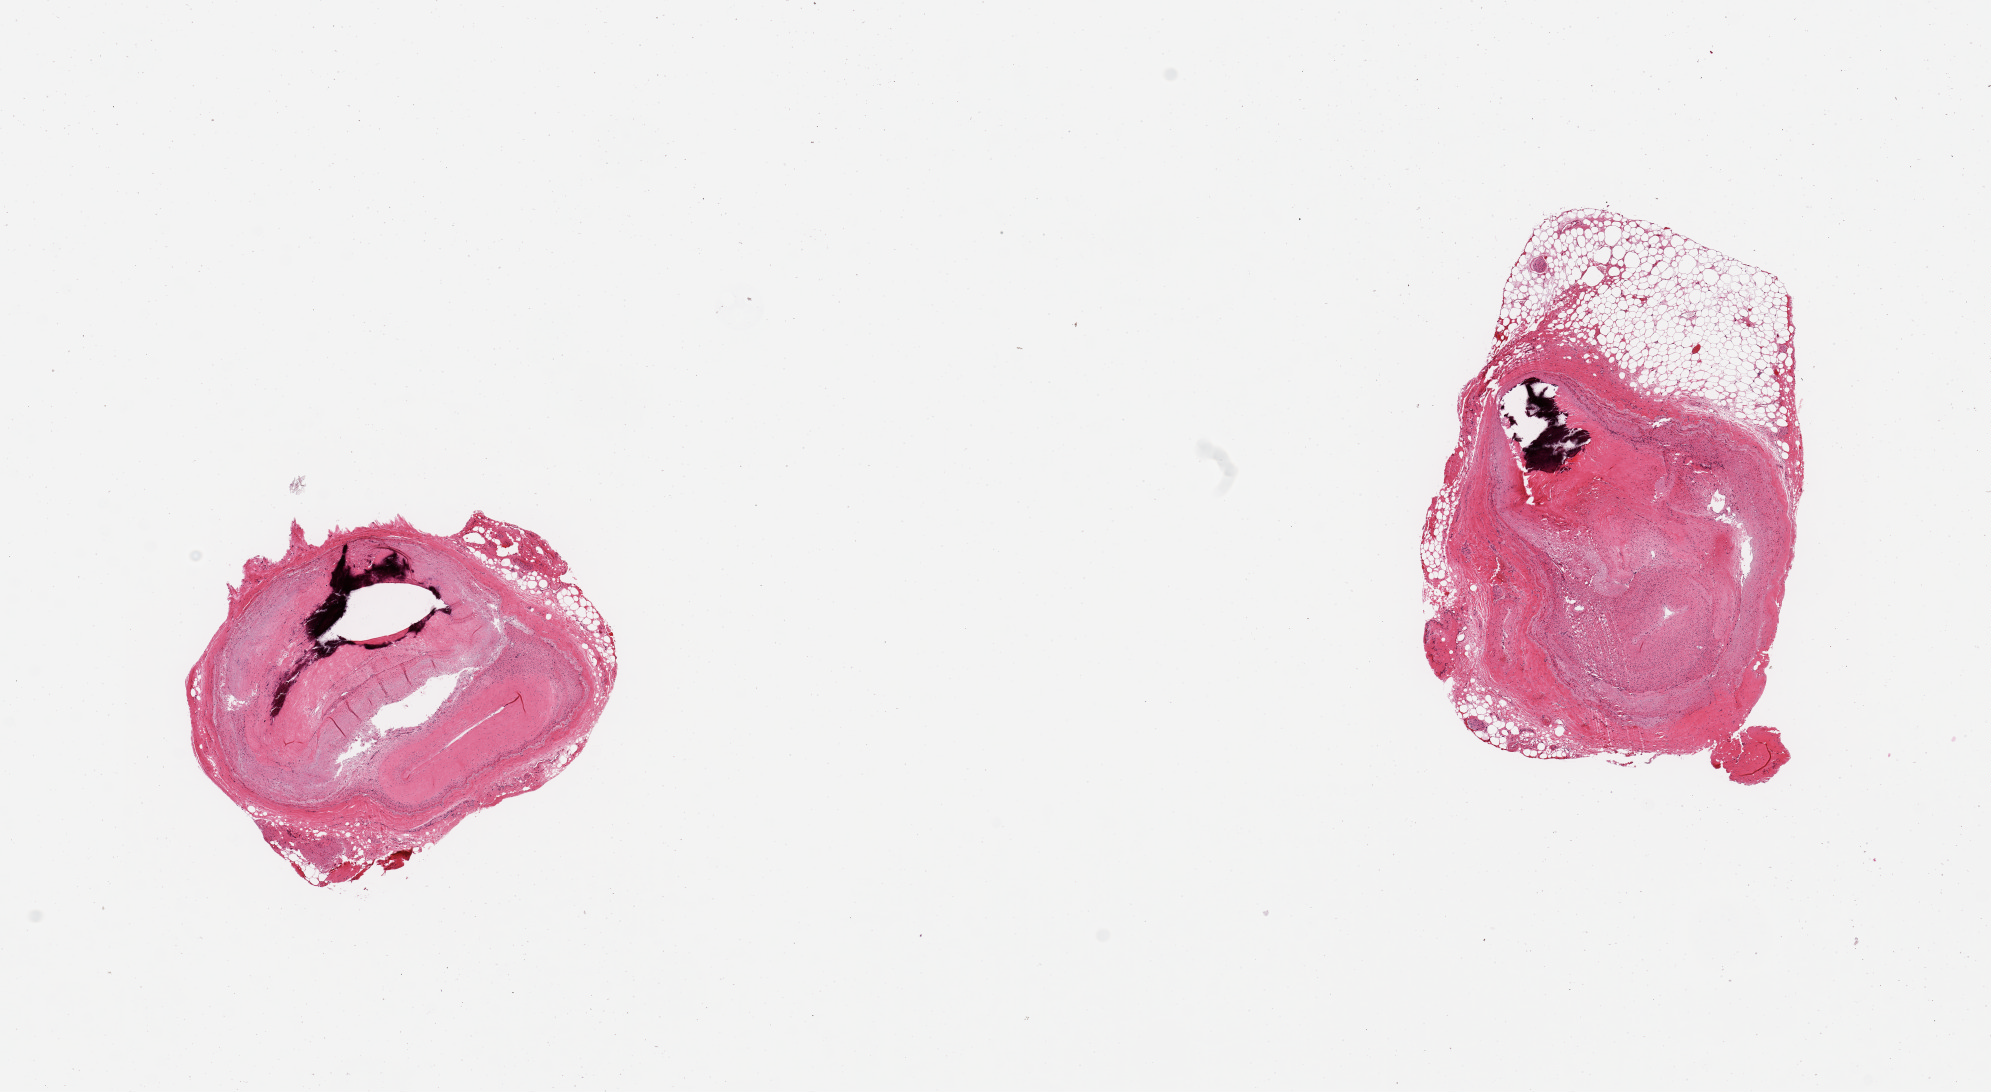
Whole-slide image, H&E stain — a low-resolution overview of the entire scanned area, about 15.8 x 8.6 mm (acquisition: 20x scan), PAXgene-fixed paraffin-embedded (PFPE) section, sampled site (target tissue): coronary artery, donor tissue sample.
Pathologist's review note for this sample: 2 pieces, sub-totally occlusive calcified atherosis; nubbin of adherent fat up to ~1mm.